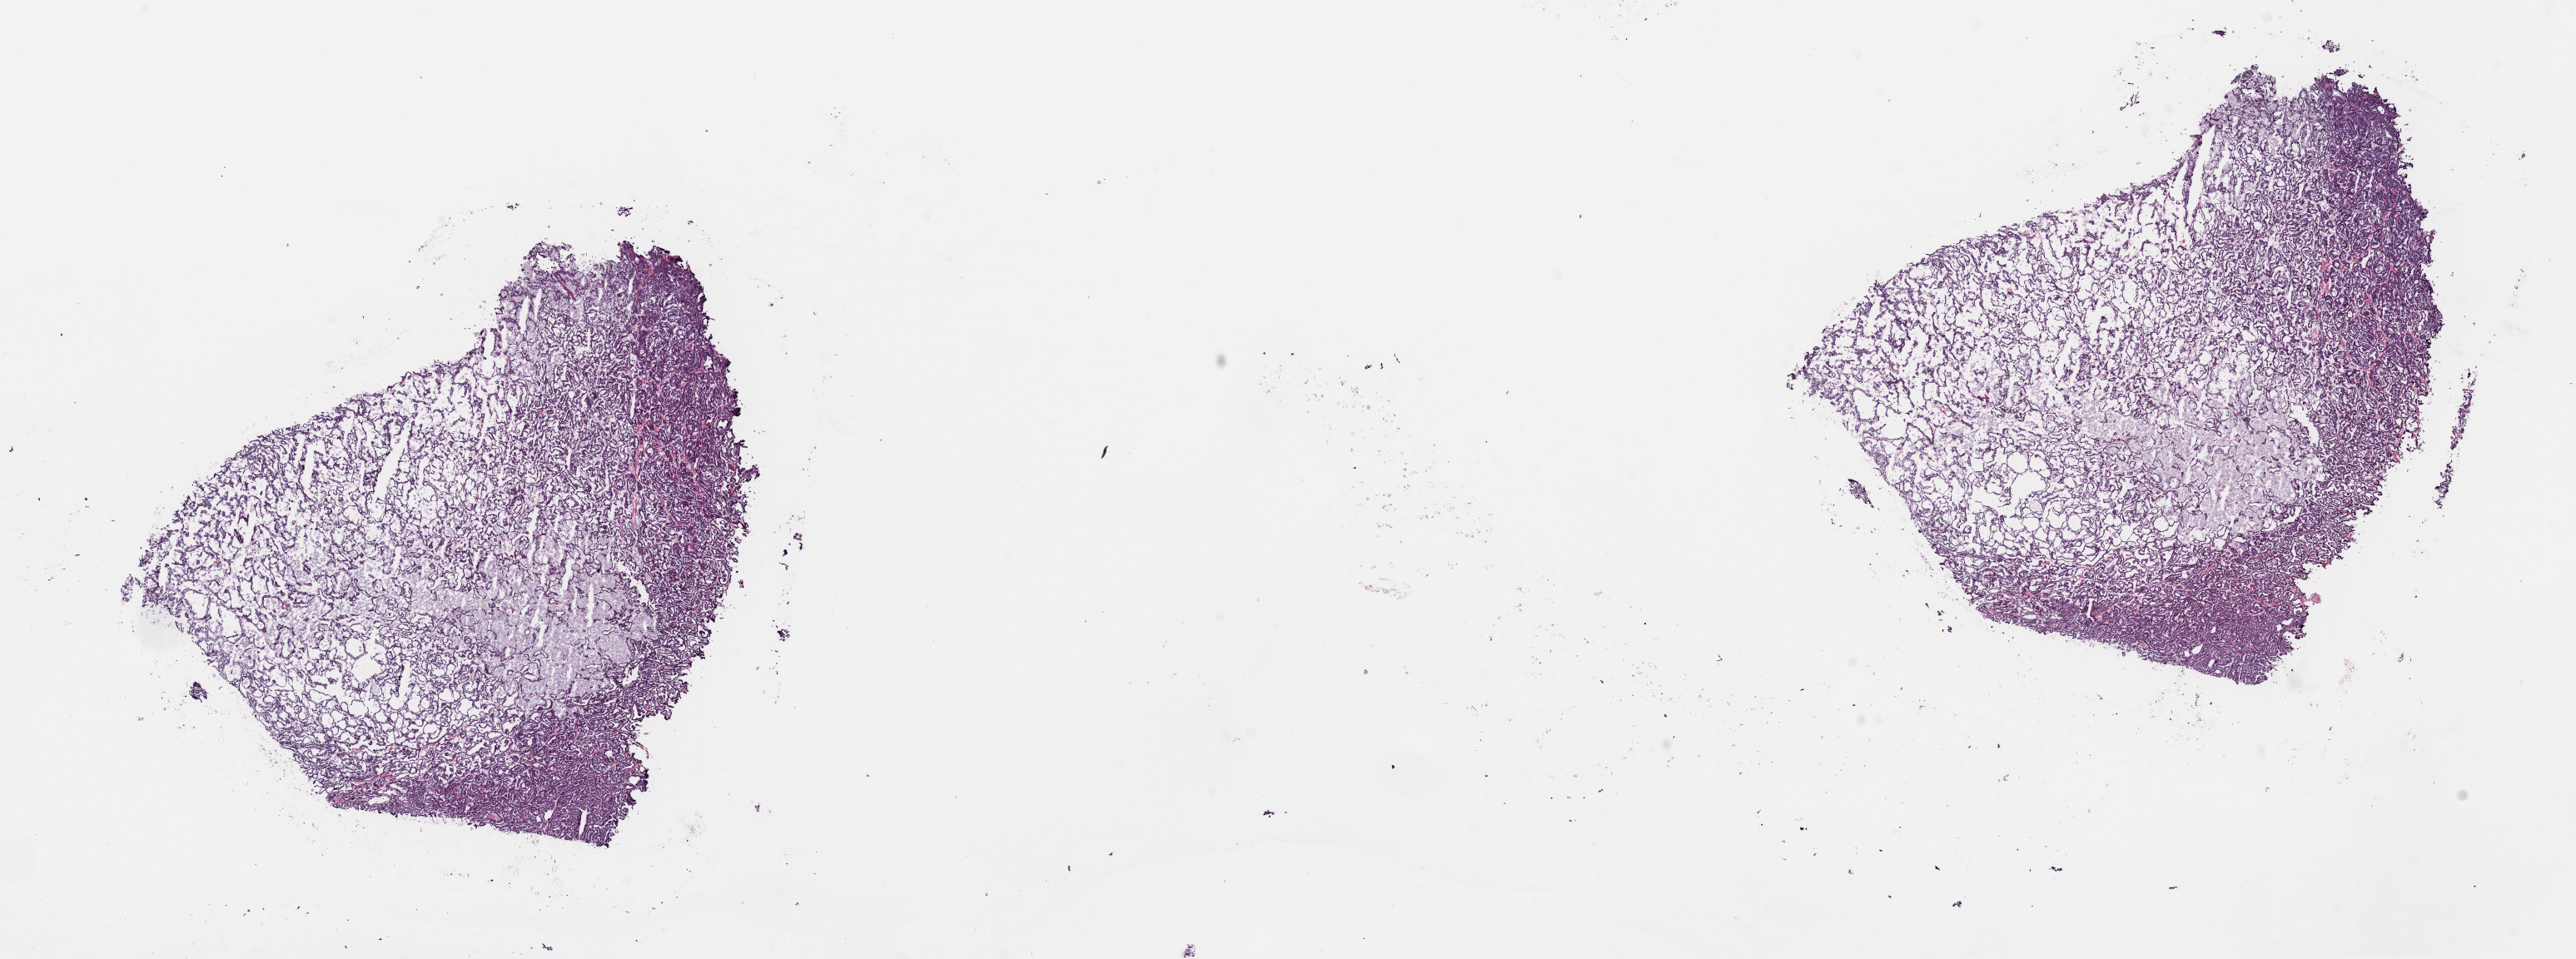
Whole-slide histology image, H&E-stained — a low-resolution overview of the entire scanned area, about 24.4 x 9.1 mm (acquisition: 40x scan). Frozen section from the top of the tissue portion. Sample: primary tumour, kidney. Patient: female, age at initial diagnosis 71 years. Composition of this section per pathologist review: tumour cells 70%, tumour nuclei 90%, normal cells 0%, stromal cells 10%, necrosis 20%. Inflammatory infiltration, as recorded: lymphocyte infiltration 50%, monocyte infiltration 50%, neutrophil infiltration 0%.
AJCC pathologic stage: I (7th edition). Diagnosis: Papillary adenocarcinoma, NOS. Laterality: left.